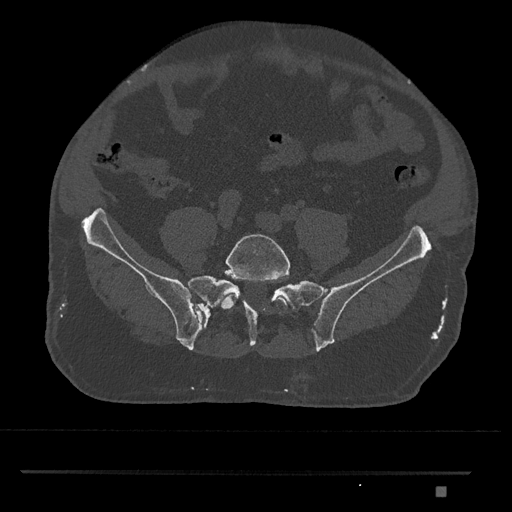
CT including the spine, one axial slice; position 530 of 1134 along the scan axis; 120 kVp; bone window (W 1800 / L 400 HU); 0.5 mm slice thickness; 512 × 512 image matrix, field of view 429 × 429 mm. Patient: male, 65 years. From the clinical record (not read from this slice): primary cancer: prostate.
Outlined on this slice (semi-automatically segmented with operator editing):
- L5 vertebra: bounding box <221,234,291,312> (left, top, right, bottom; pixels)